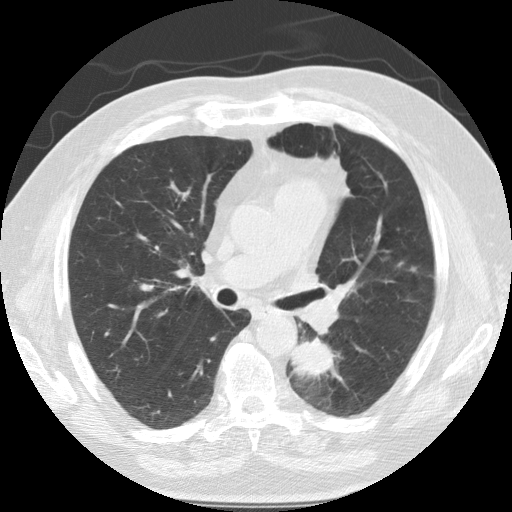
Low-dose screening chest CT, one axial slice; position 70 of 124 along the scan axis; reconstruction kernel STANDARD; 120 kVp; lung window (W 1500 / L -600 HU); 2.5 mm slice thickness; 512 × 512 image matrix.
Outlined on this slice (manually delineated by an expert):
- lesion 1 (tumor, lower lobe of left lung): bounding box [x1, y1, x2, y2] px = [290, 337, 335, 381]